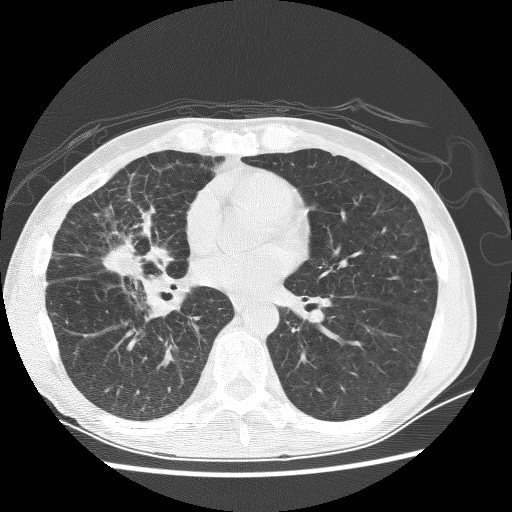
Axial slice from a low-dose chest CT screening exam. Baseline annual screen. Lung window (W 1500 / L -600 HU). Lung (sharp) reconstruction kernel (BONE). Slice 137 of 256 in the series. 512 × 512 image matrix. Male, age 67 years at enrolment. Current smoker at enrolment.
• Expert reader's lesion annotation, bounding box <80,220,174,291> (left, top, right, bottom; pixels).
• The exam's reader record, not a measurement of the box and not confirmed to be the same lesion: non-calcified nodule or mass ≥4 mm, right middle lobe, 28 × 18 mm, spiculated (stellate) margins, soft tissue attenuation.
• Official screen result: positive, change unspecified: nodule(s) >= 4 mm or enlarging nodule(s), mass(es), or other non-specific abnormalities suspicious for lung cancer.
• Participant outcome: lung cancer diagnosed 69 days after this screen — adenocarcinoma, NOS, right middle lobe, stage IV (AJCC 6th edition), 60 mm at pathology.